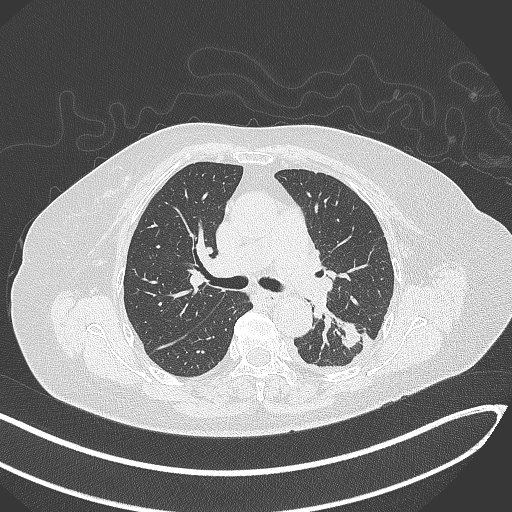
Chest CT, one axial slice; position 197 of 270 along the scan axis; reconstruction kernel B70f; 120 kVp; lung window (W 1500 / L -600 HU); 1 mm slice thickness; 512 × 512 image matrix, field of view 400 × 400 mm. Patient: female, 76 years. Case-level facts recorded for this patient, not image findings: clinical TNM (as recorded): T1c N0 M0.
Outlined on this slice (bounding box drawn by a radiologist):
- lung tumour (recorded histology: adenocarcinoma): bounding box (x1, y1, x2, y2) in pixels: (337, 318, 359, 352)